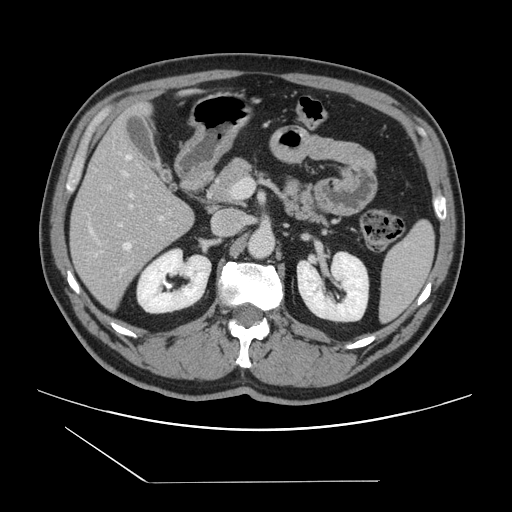
Contrast-enhanced abdominal CT, one axial slice; slice 72 of 157 in the series (ordered by position); 120 kVp; soft-tissue window (W 400 / L 40 HU); 2.5 mm slice thickness; 512 × 512 image matrix, field of view 407 × 407 mm. Male patient, age 61 years. From the clinical record (not read from this slice): diagnosis: colorectal cancer liver metastases, imaged before liver resection; multiple liver metastases: yes; largest metastasis: 5.5 cm; disease in both lobes: yes.
Structures marked on this image (expert manual segmentation):
- hepatic veins: bounding box [x1, y1, x2, y2] px = [90, 155, 133, 250]
- liver: [71, 106, 194, 308]
- planned liver remnant (the part of the liver to remain after resection): [72, 105, 197, 220]
- portal vein (with intrahepatic branches): [120, 172, 164, 226]